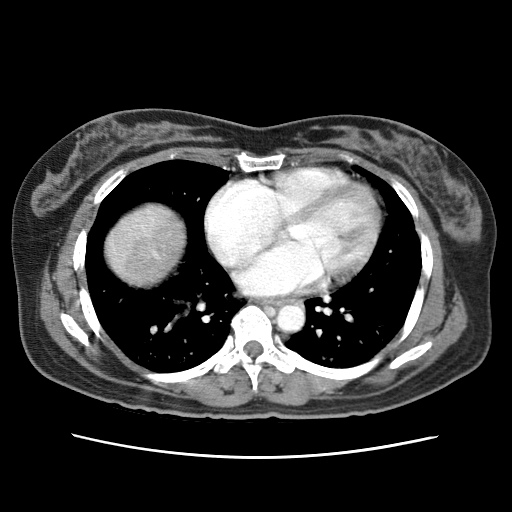
Contrast-enhanced abdominal CT (liver protocol), one axial slice; position 72 of 79 along the scan axis; reconstruction kernel STANDARD; 120 kVp; soft-tissue window (W 400 / L 40 HU); 2.5 mm slice thickness; 512 × 512 image matrix. From the clinical record (not read from this slice): diagnosis: hepatocellular carcinoma (patient treated with transarterial chemoembolisation; whether this scan precedes or follows treatment is not stated here); TNM stage (as recorded): Stage-I; Child-Pugh class: A; tumour differentiation: moderately differentiated; tumour nodularity: uninodular.
Structures marked on this image (semi-automatically segmented with operator editing):
- abdominal aorta: bounding box <276,304,303,332> (left, top, right, bottom; pixels)
- liver parenchyma outside the tumour (the mass and vessels are separate outlines, so this box may not span the whole liver): <106,204,184,284>